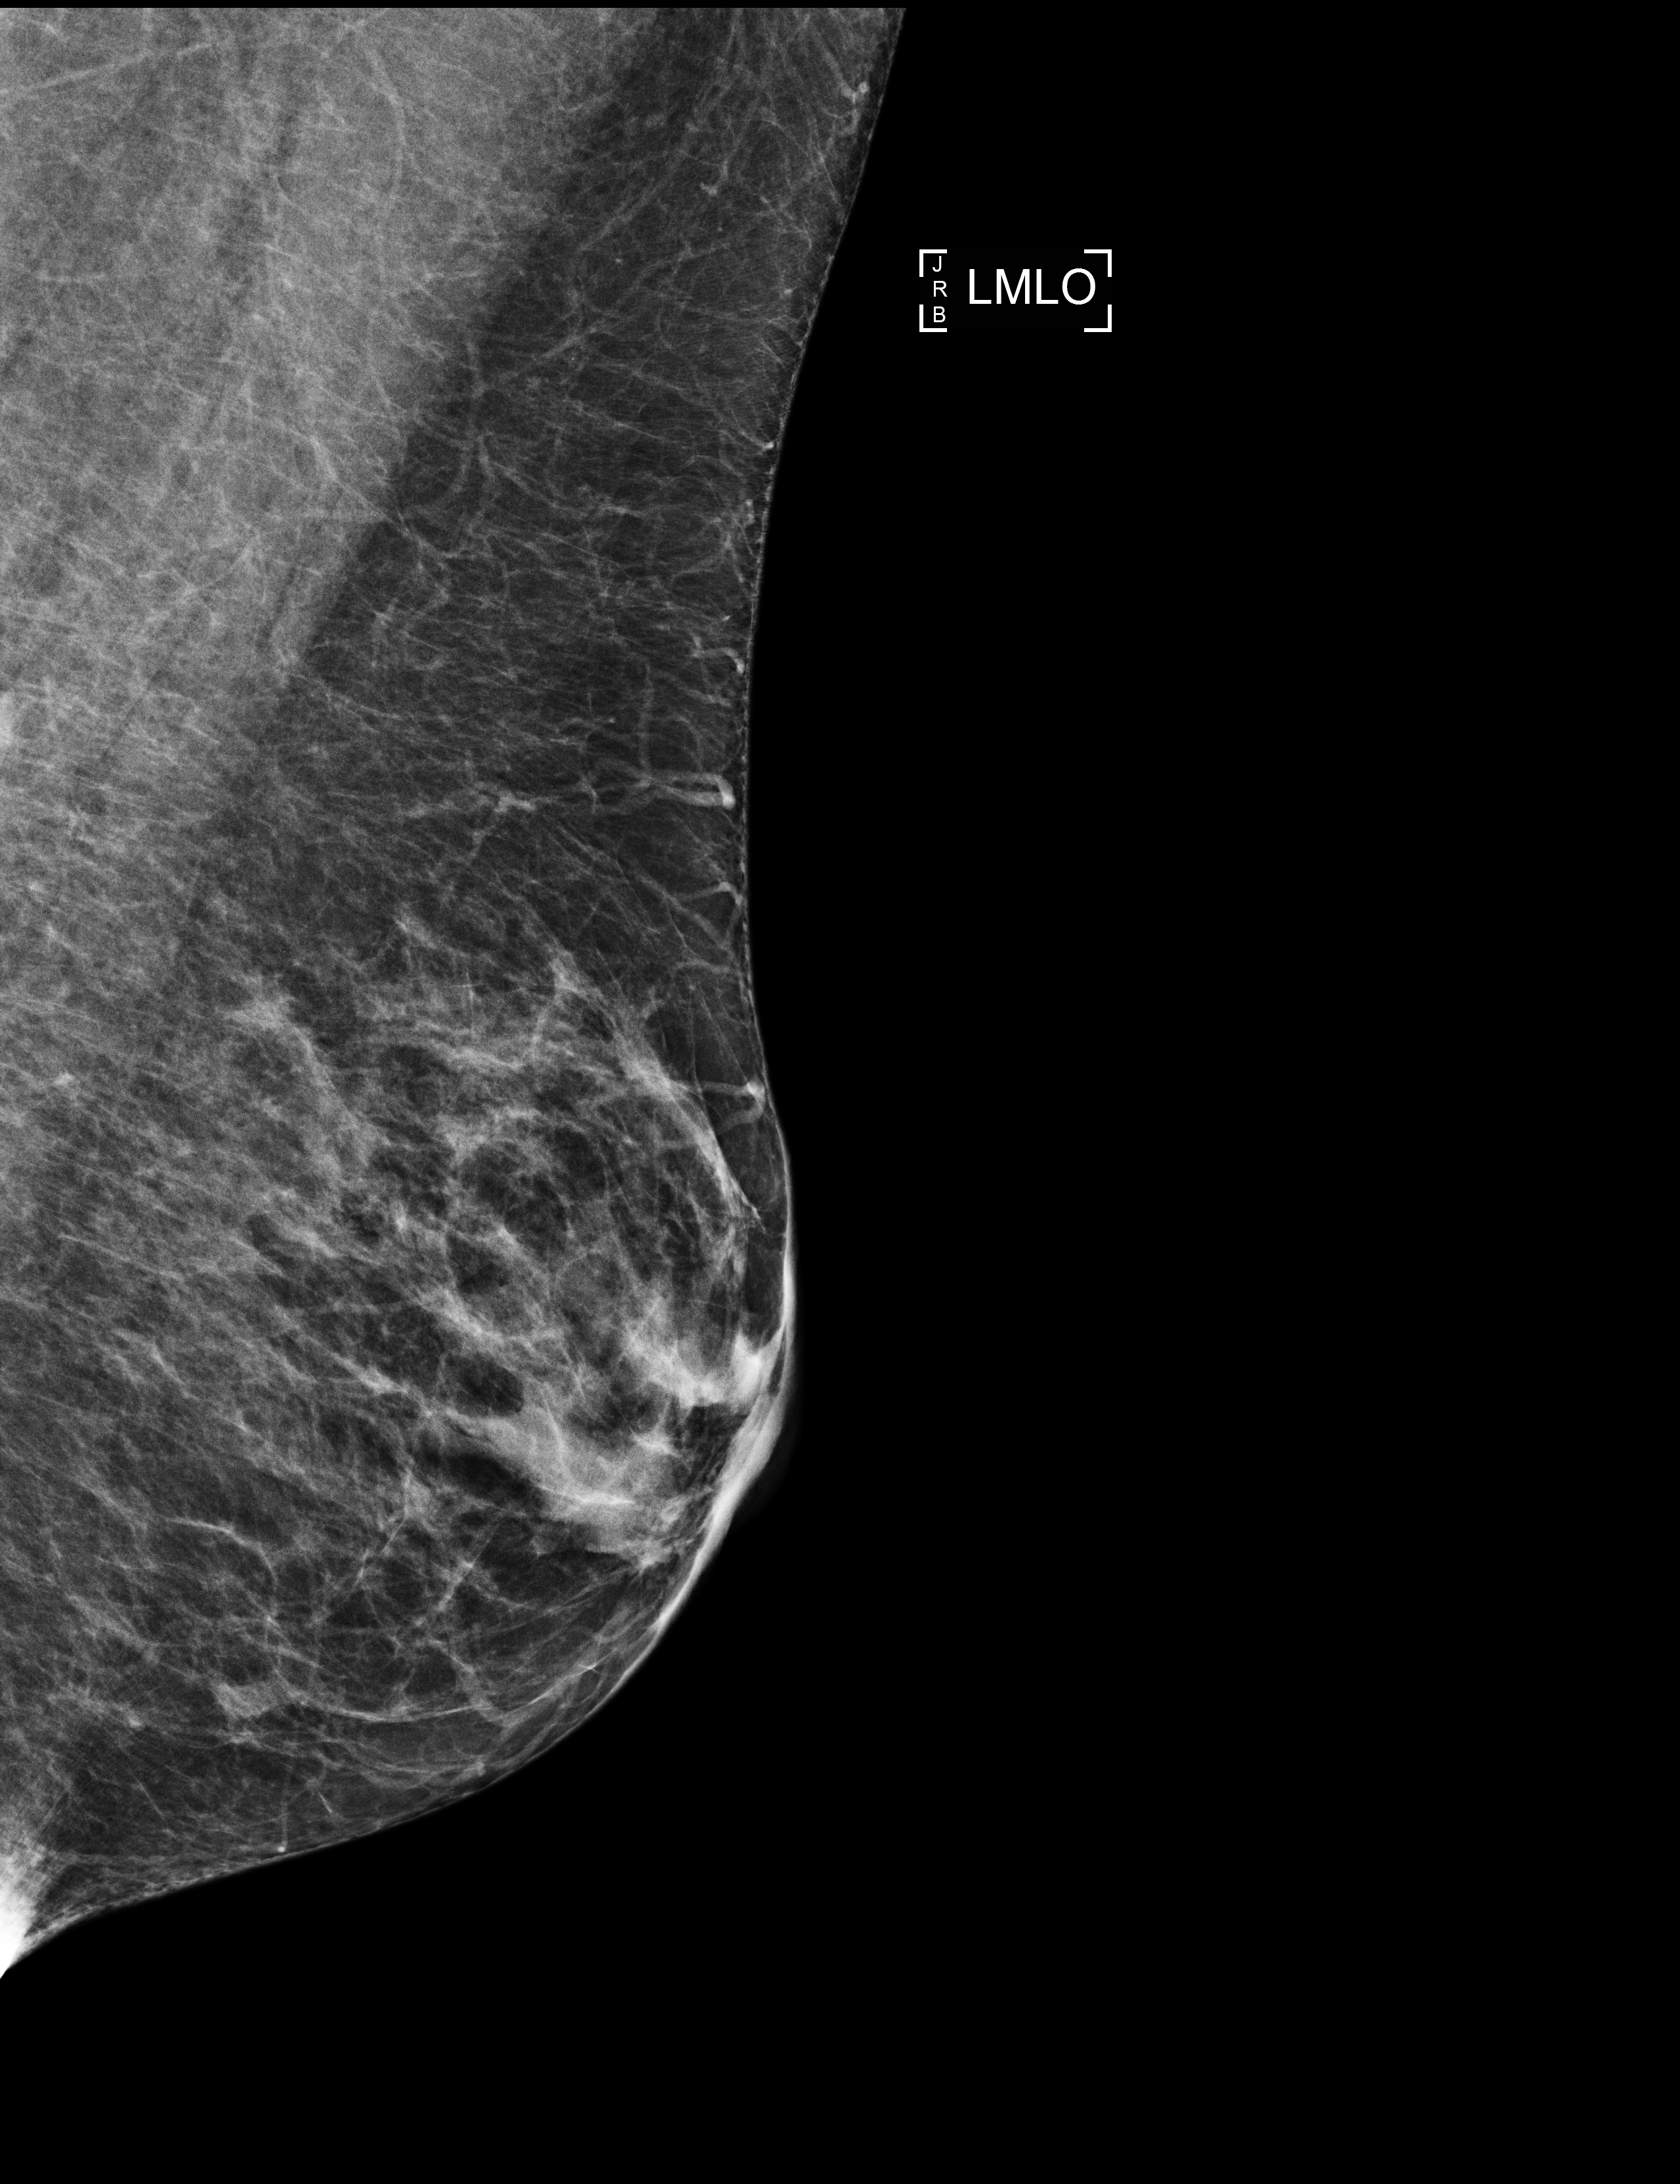
Screening examination. Patient aged 60 years (female).
Image type: full-field digital mammogram. Breast: left. Projection: MLO view.